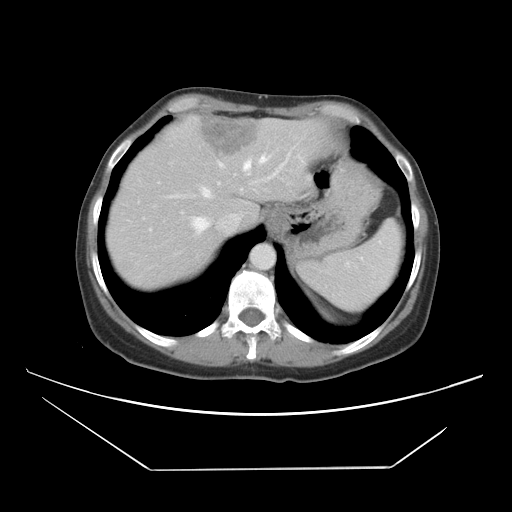
Contrast-enhanced abdominal CT, one axial slice; position 34 of 42 along the scan axis; 120 kVp; intravenous contrast given; soft-tissue window (W 400 / L 40 HU); 512 × 512 image matrix, field of view 399 × 399 mm. Female patient, age 52 years. Case-level facts recorded for this patient, not image findings: diagnosis: colorectal cancer liver metastases, imaged before liver resection; multiple liver metastases: yes; largest metastasis: 5.5 cm; disease in both lobes: yes.
Structures marked on this image (manually delineated by an expert):
- hepatic veins: bounding box <150,154,271,234> (left, top, right, bottom; pixels)
- liver: <109,117,321,288>
- planned liver remnant (the part of the liver to remain after resection): <123,127,235,224>
- portal vein (with intrahepatic branches): <181,143,299,214>
- liver metastasis: <201,120,256,154>